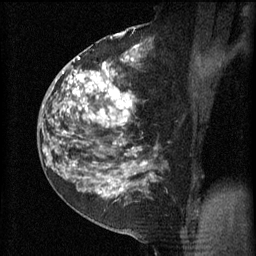
Breast MRI (dynamic contrast-enhanced), one sagittal slice. Slice 28 of 60 in the series (ordered by position). 3 images stored at this slice position (order not interpretable as contrast timing). 1.5 T. TE 4.2 ms, TR 11 ms. 2 mm slice thickness. 256 × 256 image matrix, field of view 180 × 180 mm. Female patient, age 52 years.
Outlined on this slice (semi-automatic segmentation, software-assisted and operator-edited):
- analysis volume of interest (the breast-tissue region the enhancement analysis was run in; not a lesion): bounding box [x1, y1, x2, y2] px = [81, 52, 143, 157]
- tumour enhancement mask (voxels above the 70 % enhancement threshold inside the analysis volume of interest): [81, 58, 138, 157]